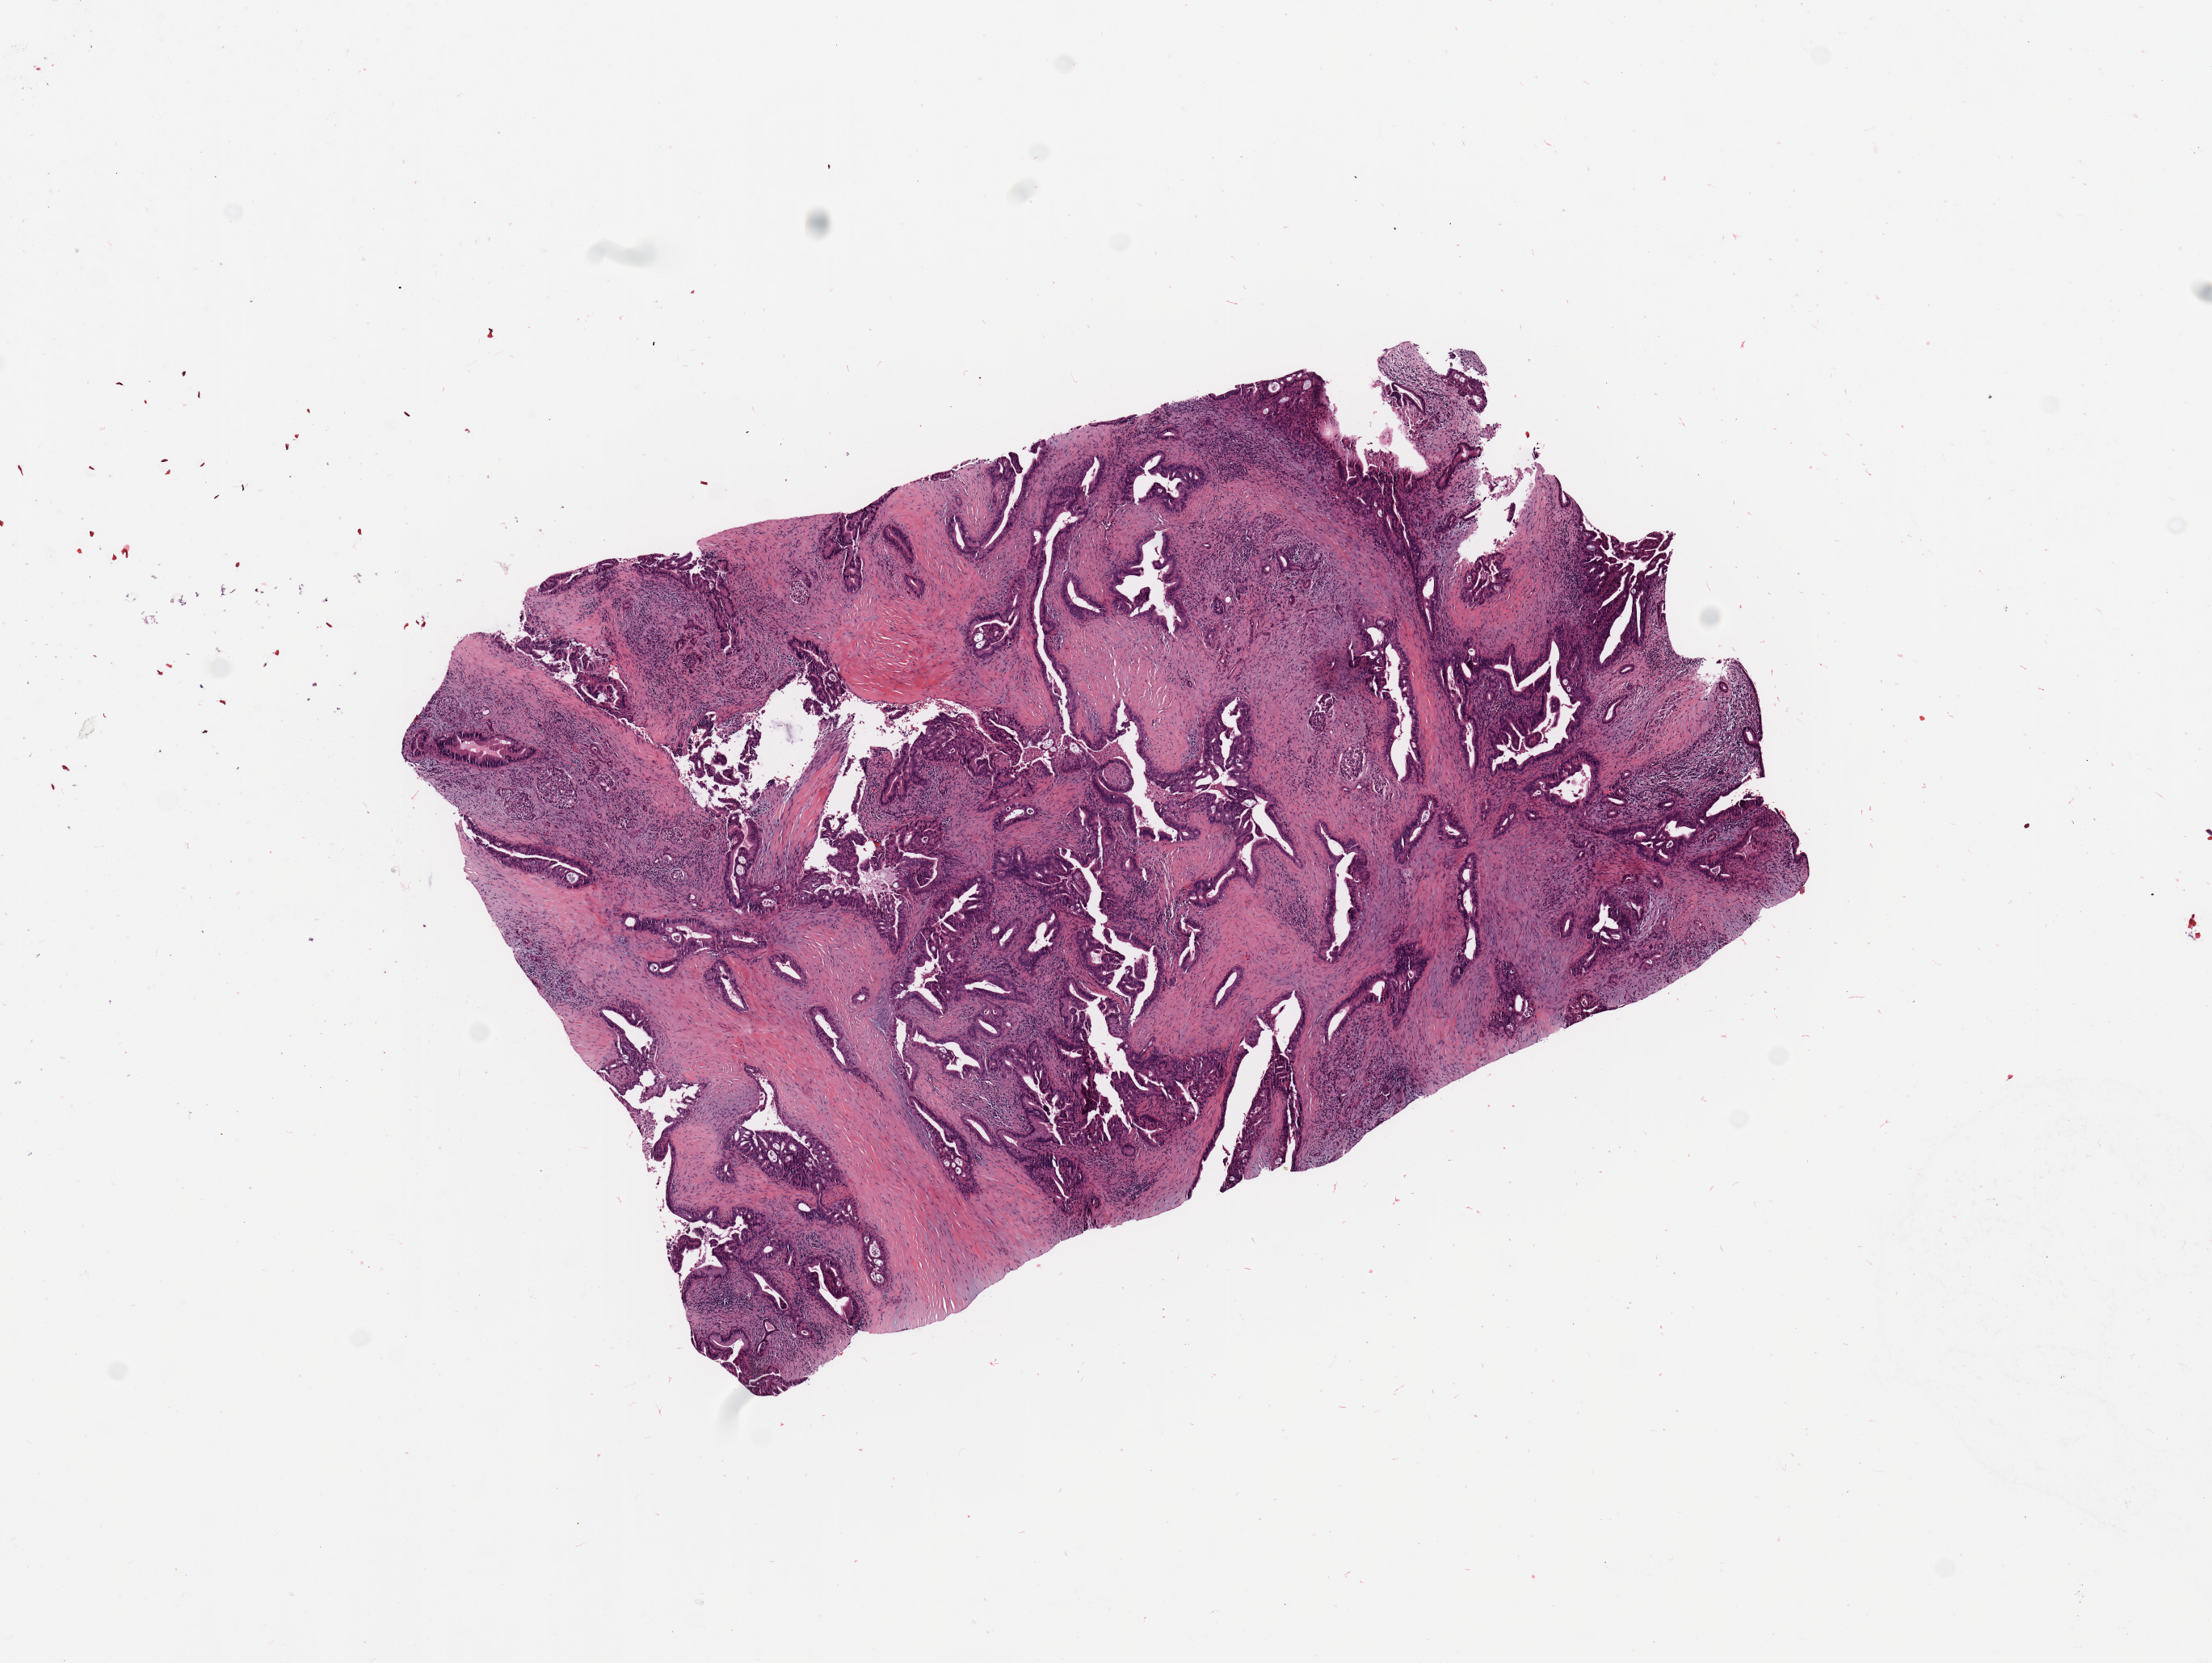
Whole-slide histology image, Hematoxylin and eosin (H&E) stained — shown as a low-resolution overview of the whole scanned area (about 10.8 x 8.1 mm), tumour tissue sample, sampled site: pancreas. Male, 63 y/o. Histologic grade: G2 (moderately differentiated). Composition of this section per pathologist review: tumour nuclei 70%, necrosis 0%.
Histologic diagnosis: Infiltrating duct carcinoma, NOS. Primary tumour site (as recorded): head. AJCC pathologic stage: IB.